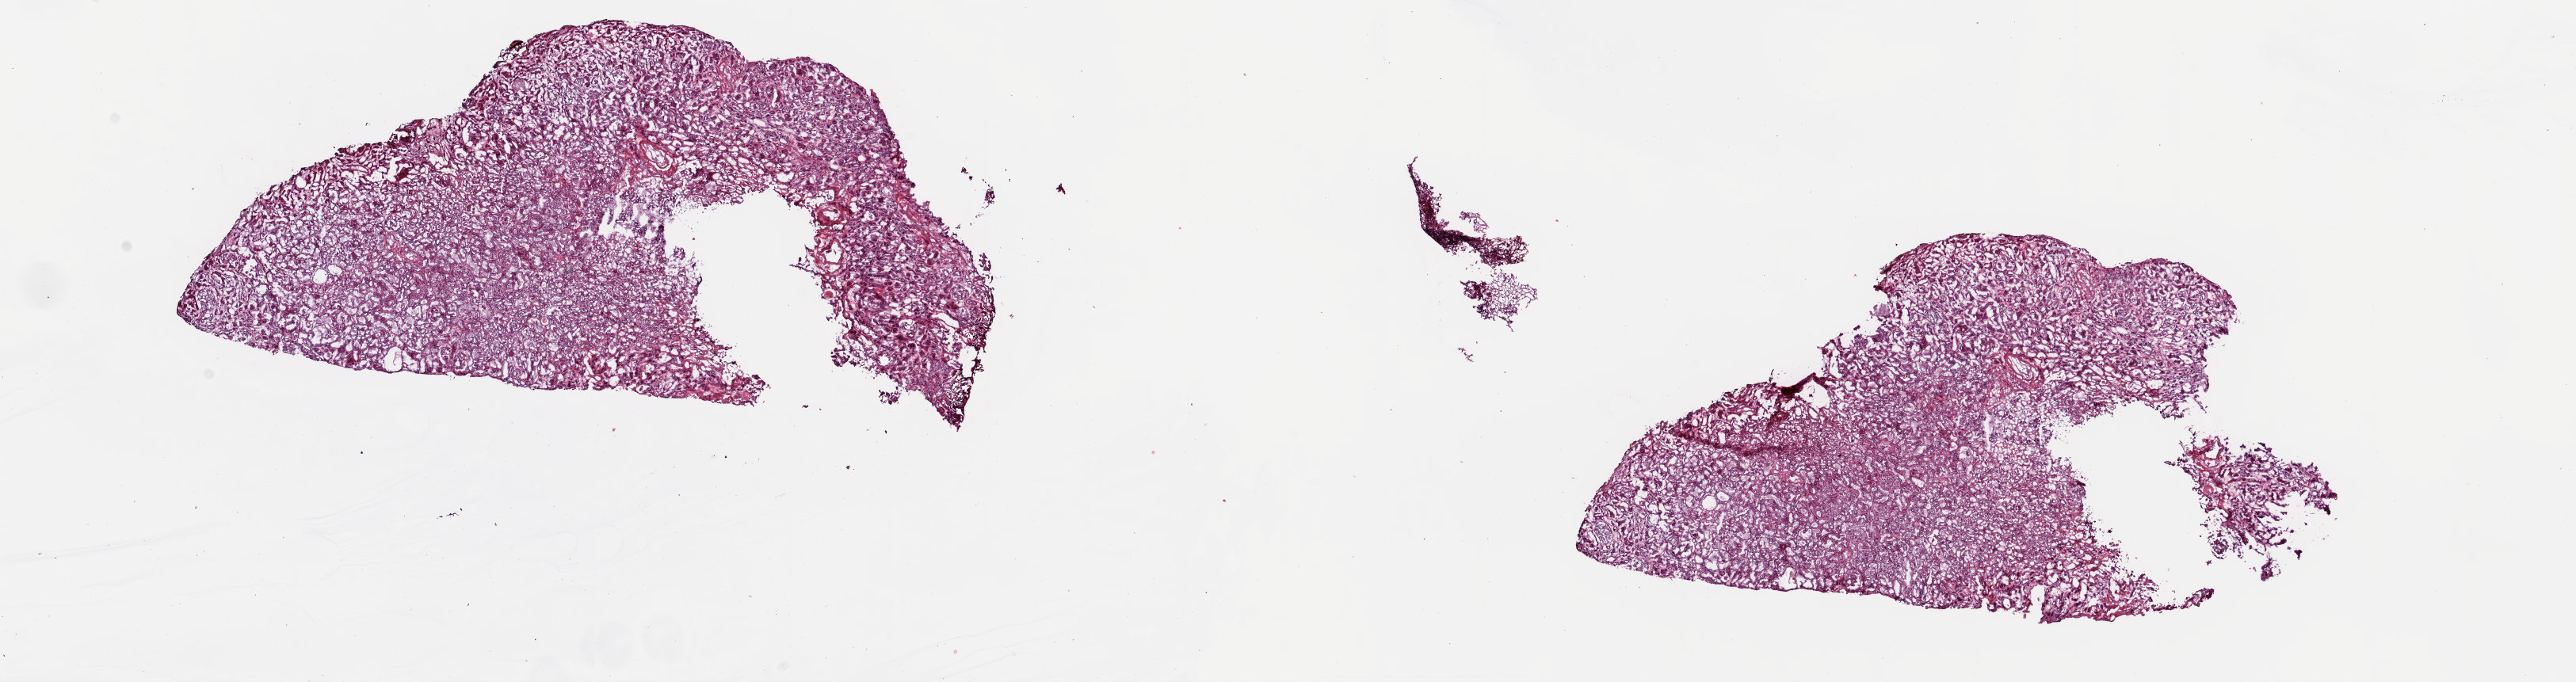
Digitized H&E-stained tissue section (whole slide) — whole scanned area (about 25.8 x 6.8 mm) shown as a low-resolution overview, frozen section from the top of the tissue portion, sample: solid tissue normal (non-tumour tissue), kidney. Patient: male, age at initial diagnosis 69 years. Slide review estimates, as recorded: tumour cells 0%, tumour nuclei 0%, normal cells 50%, stromal cells 50%, necrosis 0%. Infiltration values recorded for this section: lymphocyte infiltration 3%, monocyte infiltration 0%, neutrophil infiltration 0%.
This section: solid tissue normal (non-tumour) sample from the same patient. Patient diagnosis: Papillary adenocarcinoma, NOS.